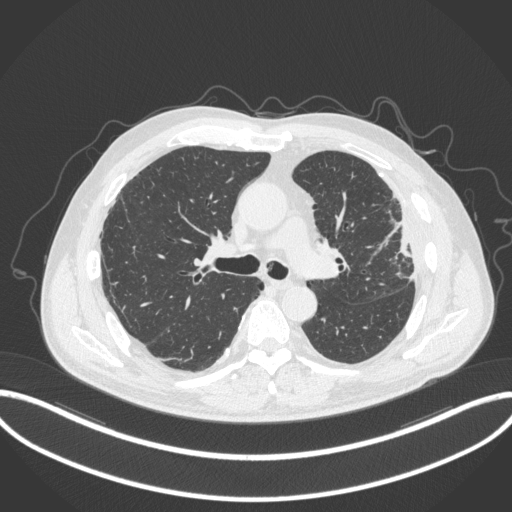
Chest CT, one axial slice. Reconstruction kernel B31f. 120 kVp. Lung window (W 1500 / L -600 HU). 512 × 512 image matrix, field of view 415 × 415 mm. Male patient, age 64 years. Case-level facts recorded for this patient, not image findings: clinical TNM (as recorded): T4 N1 M0; histopathological grade: G3.
Annotated regions visible in this slice (bounding box drawn by a radiologist):
- lung tumour (recorded histology: adenocarcinoma): box from (x=390, y=220) to (x=415, y=261) px